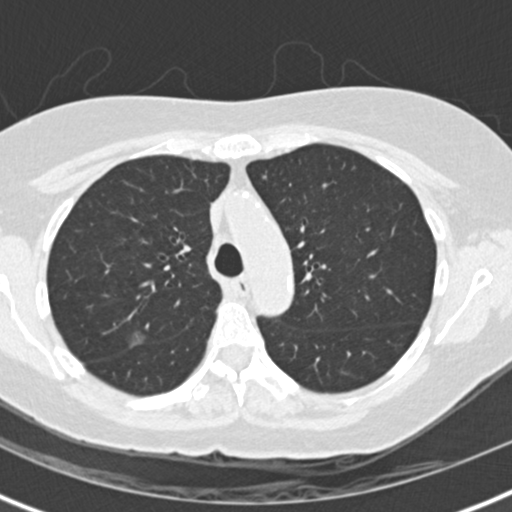
Low-dose screening chest CT, one axial slice; position 100 of 147 along the scan axis; reconstruction kernel B30f; 120 kVp; lung window (W 1500 / L -600 HU); 2 mm slice thickness; 512 × 512 image matrix.
Outlined on this slice (manually delineated by an expert):
- lesion 1 (tumor, upper lobe of right lung): box from (x=130, y=331) to (x=146, y=348) px